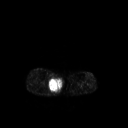
FDG PET of an extremity soft-tissue mass (from a PET/CT study), one axial slice; slice 140 of 267 in the series (ordered by position); 128 × 128 image matrix, field of view 500 × 500 mm. Patient: male, 69 years. Case-level facts recorded for this patient, not image findings: histological type: pleiomorphic liposarcoma; grade: high; site of the primary tumour: right calf.
Structures marked on this image (expert contour drawn on MRI and transferred to this co-registered scan by the dataset authors):
- gross tumour volume including surrounding oedema: bounding box <49,76,62,92> (left, top, right, bottom; pixels)
- gross tumour volume (mass): <49,77,63,91>